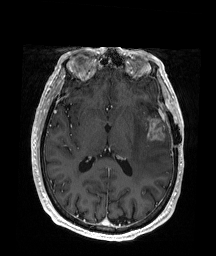
Brain MRI from a brain-tumour surgery series, one axial slice. Position 92 of 176 along the scan axis. T1-weighted post-contrast. 1 mm slice thickness. 216 × 256 image matrix, field of view 219 × 260 mm. From the clinical record (not read from this slice): histopathology: Glioblastoma; WHO grade: 4.
Annotated regions visible in this slice (expert manual segmentation):
- tumour: bounding box [x1, y1, x2, y2] px = [146, 116, 166, 141]